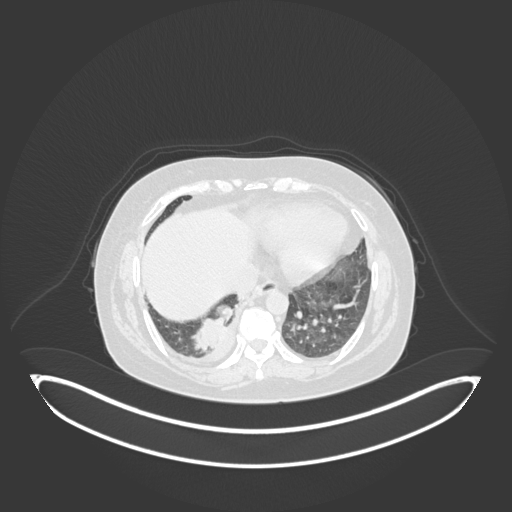
Chest CT, one axial slice. Slice 36 of 231 in the series (ordered by position). Reconstruction kernel B30f. 120 kVp. Lung window (W 1500 / L -600 HU). 1 mm slice thickness. 512 × 512 image matrix, field of view 500 × 500 mm. Female patient, age 56 years. Case-level facts recorded for this patient, not image findings: clinical TNM (as recorded): T2b N1 M0; histopathological grade: G3.
Annotated regions visible in this slice (rectangle marked by the reading radiologist):
- lung tumour (recorded histology: small cell carcinoma): bounding box [x1, y1, x2, y2] px = [189, 306, 239, 353]